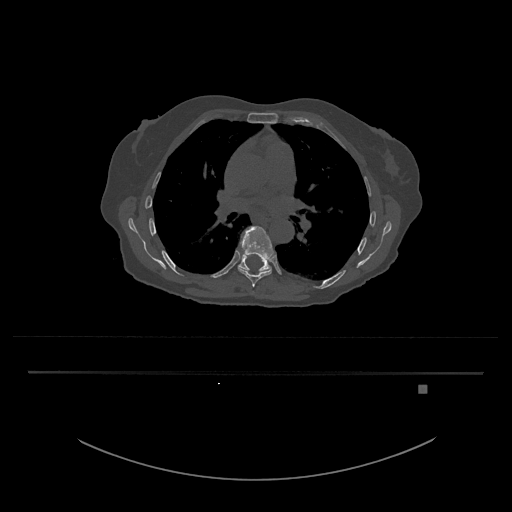
CT including the spine, one axial slice; slice 789 of 797 in the series (ordered by position); reconstruction kernel Br40s/3; bone window (W 1800 / L 400 HU); 0.5 mm slice thickness; 512 × 512 image matrix, field of view 500 × 500 mm. Female patient, age 57 years. Case-level facts recorded for this patient, not image findings: primary cancer: cervical.
Outlined on this slice (semi-automatically segmented with operator editing):
- T8 vertebra: box from (x=237, y=226) to (x=274, y=287) px
- T9 vertebra: (x=238, y=253)–(x=272, y=272)